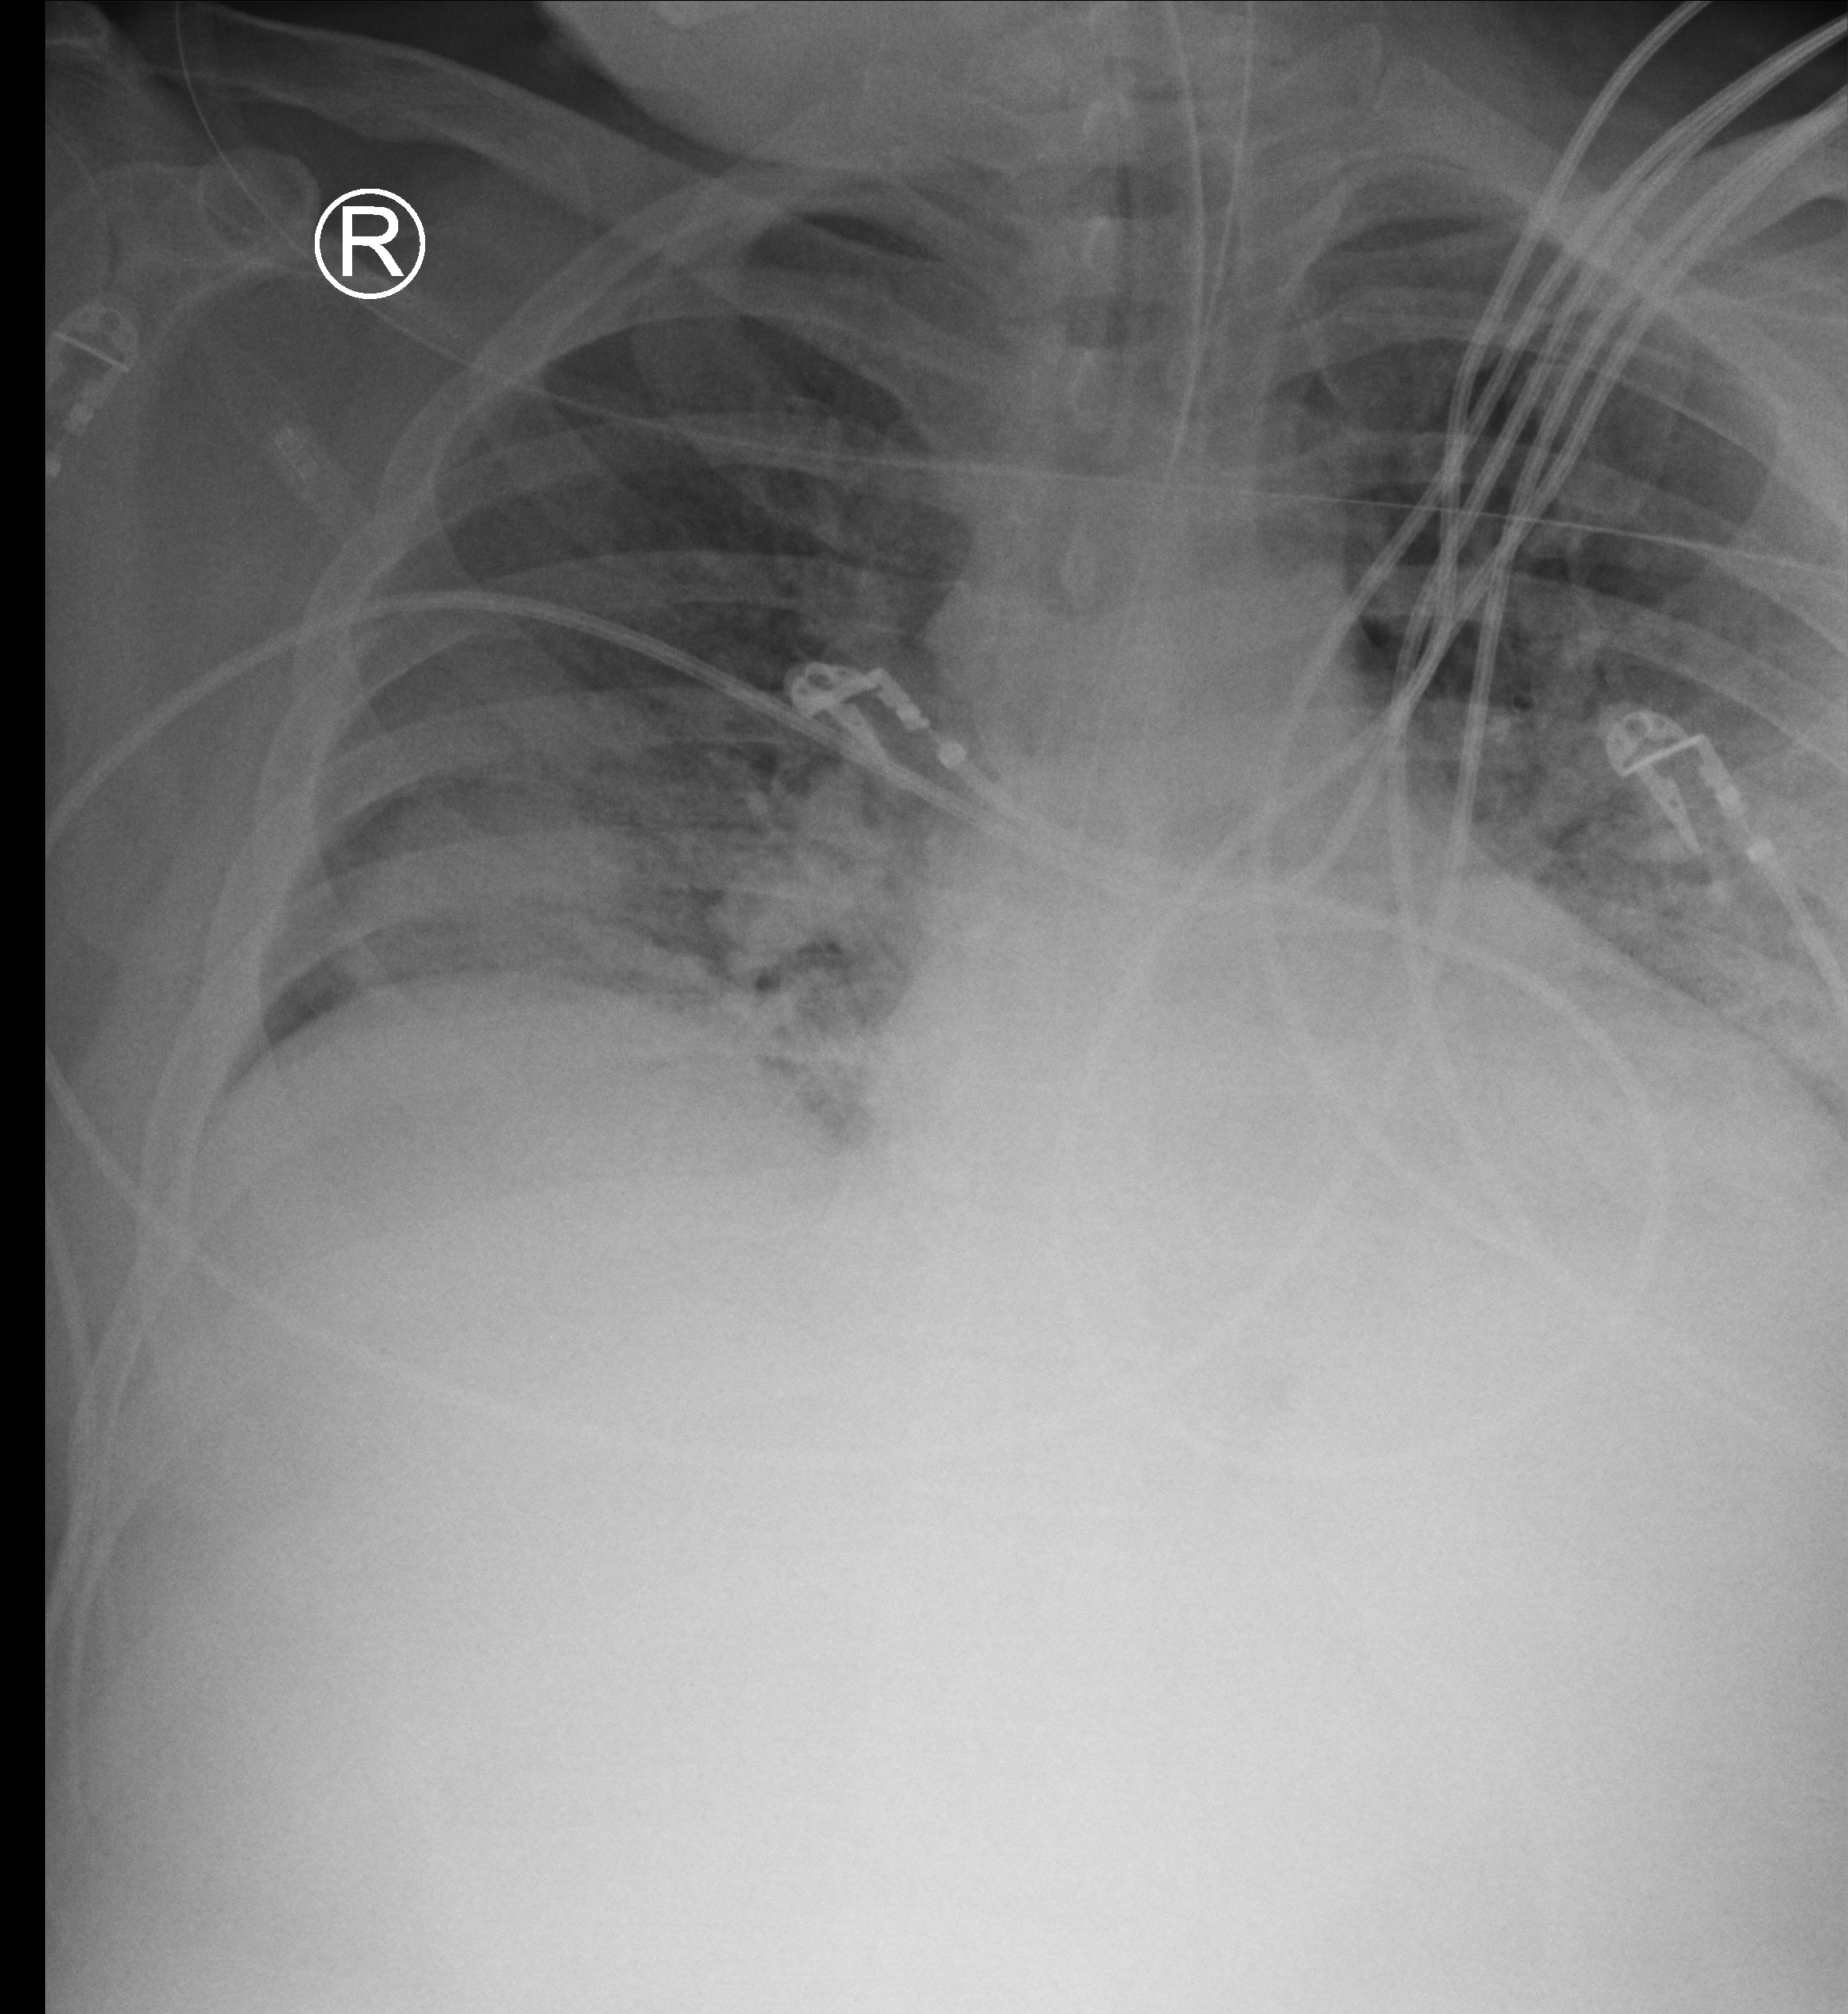
Portable chest radiograph; anteroposterior (AP) projection. Male patient hospitalised with COVID-19, age 18–59 years.
Admission-level facts for this patient (not findings on this image; timing relative to this image not recorded): admitted to intensive care during this hospital stay: yes.